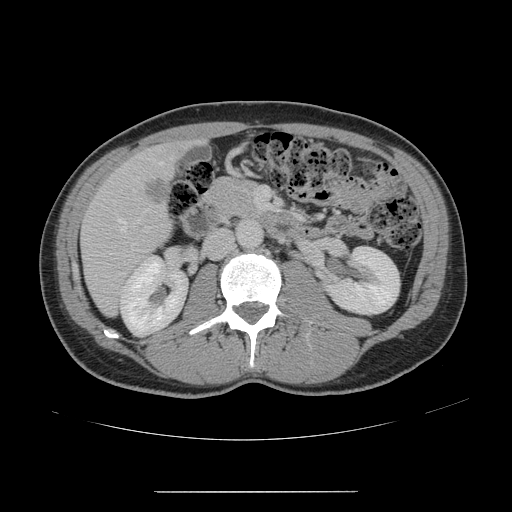
Contrast-enhanced abdominal CT, one axial slice; slice 58 of 178 in the series (ordered by position); 120 kVp; intravenous contrast given; soft-tissue window (W 400 / L 40 HU); 2.5 mm slice thickness; 512 × 512 image matrix, field of view 401 × 401 mm. Male patient, age 53 years. Case-level facts recorded for this patient, not image findings: diagnosis: colorectal cancer liver metastases, imaged before liver resection; multiple liver metastases: yes; largest metastasis: 2.4 cm; disease in both lobes: no.
Outlined on this slice (expert manual segmentation):
- hepatic veins: bounding box (x1, y1, x2, y2) in pixels: (104, 161, 162, 245)
- liver: (82, 143, 189, 313)
- portal vein (with intrahepatic branches): (255, 187, 267, 209)
- liver metastasis: (143, 179, 168, 204)